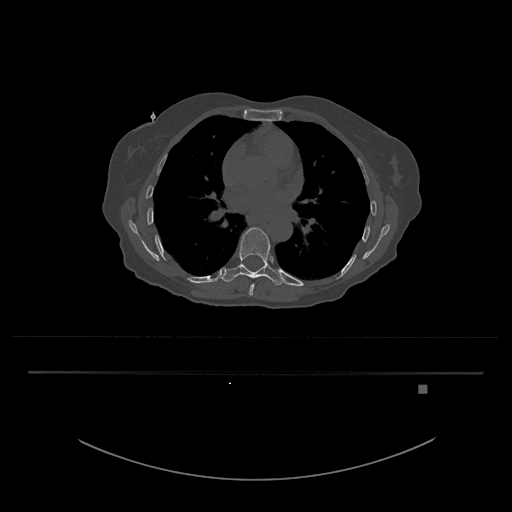
CT including the spine, one axial slice. Position 767 of 797 along the scan axis. Reconstruction kernel Br40s/3. 120 kVp. Bone window (W 1800 / L 400 HU). 0.5 mm slice thickness. 512 × 512 image matrix. Patient: female, 57 years. From the clinical record (not read from this slice): primary cancer: cervical.
Structures marked on this image (semi-automatically segmented with operator editing):
- T8 vertebra: bounding box <249,283,255,296> (left, top, right, bottom; pixels)
- T9 vertebra: <221,227,285,286>